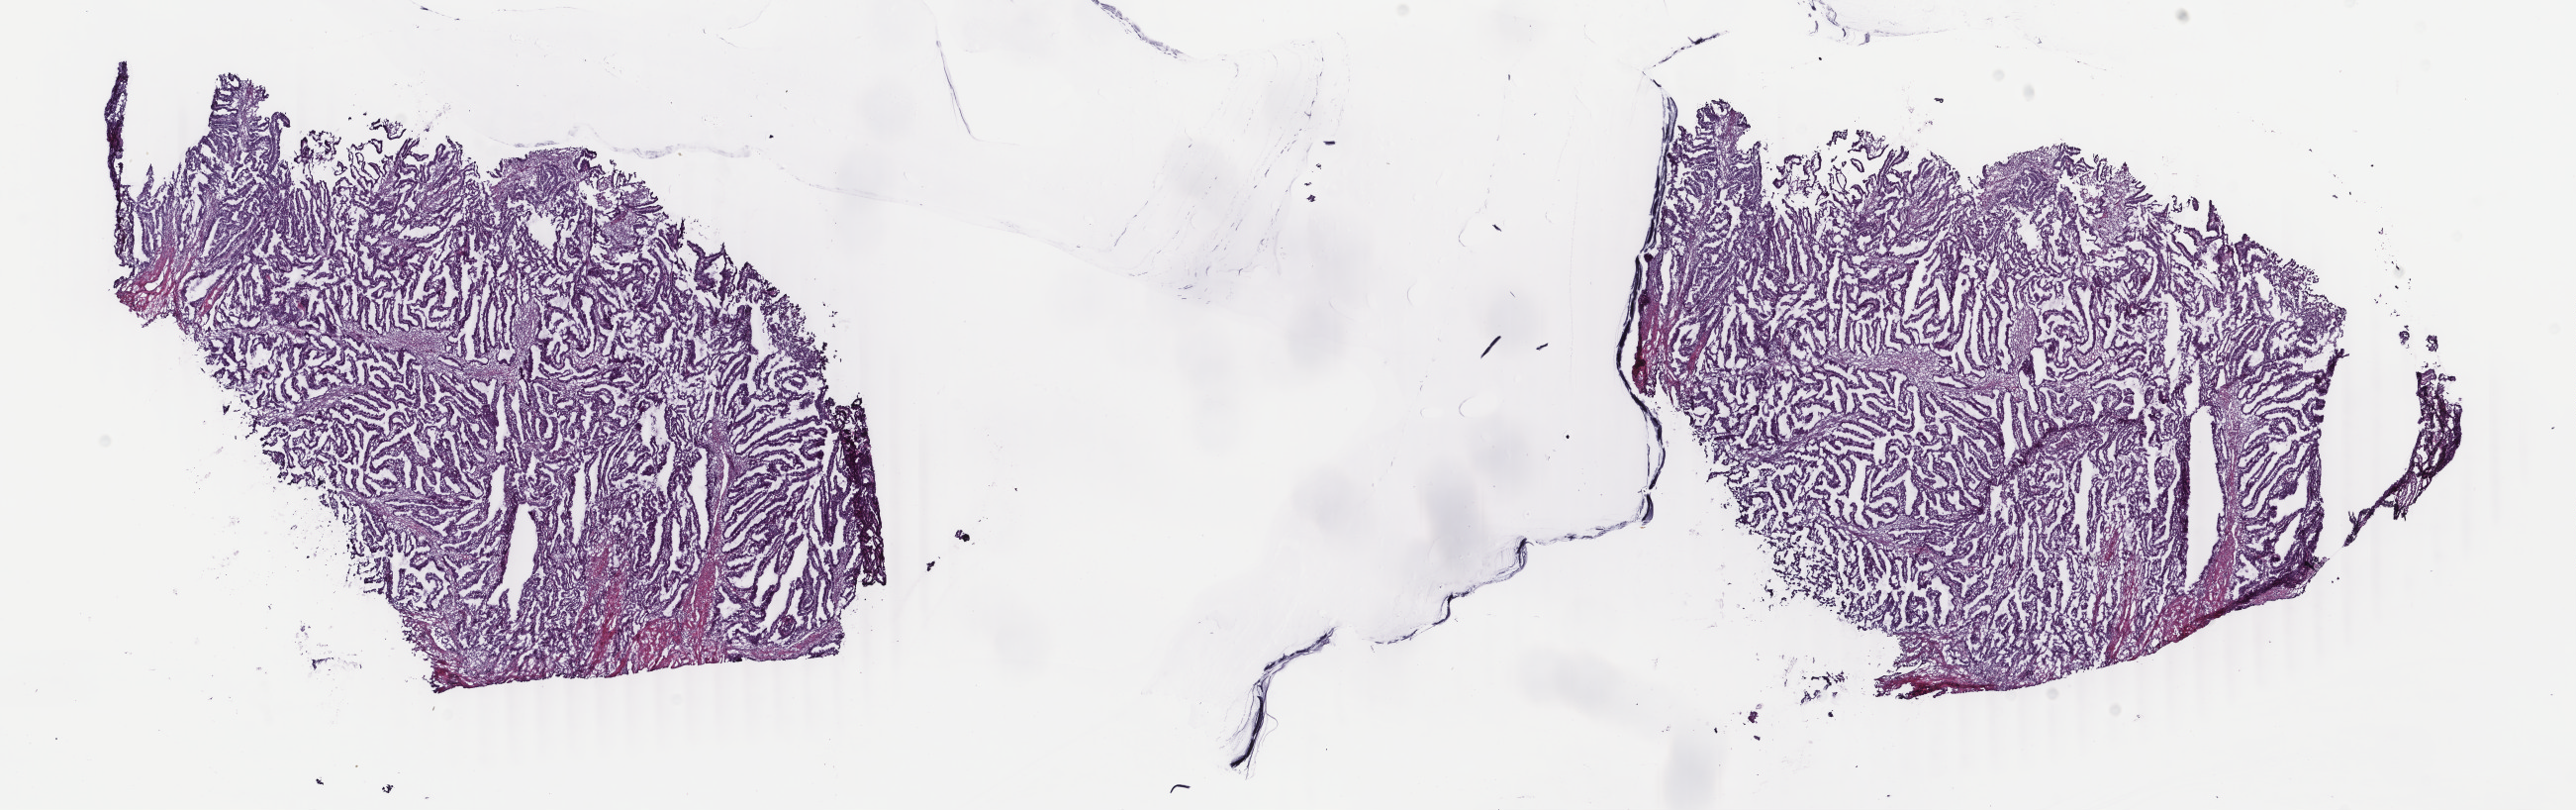
H&E-stained whole-slide image, shown as a low-resolution overview of the whole scanned area (about 20.7 x 6.5 mm, from a 40x scan), frozen section from the top of the tissue portion, primary tumour sample from the uterus. Female patient; age at initial diagnosis 56 years. Histologic grade: G1 (well differentiated). Composition of this section per pathologist review: tumour cells 75%, tumour nuclei 75%, normal cells 0%, stromal cells 25%, necrosis 0%. Infiltration values recorded for this section: lymphocyte infiltration 4%, monocyte infiltration 2%, neutrophil infiltration 1%.
• pathologic diagnosis: Endometrioid adenocarcinoma, NOS (endometrium)
• FIGO stage: IB